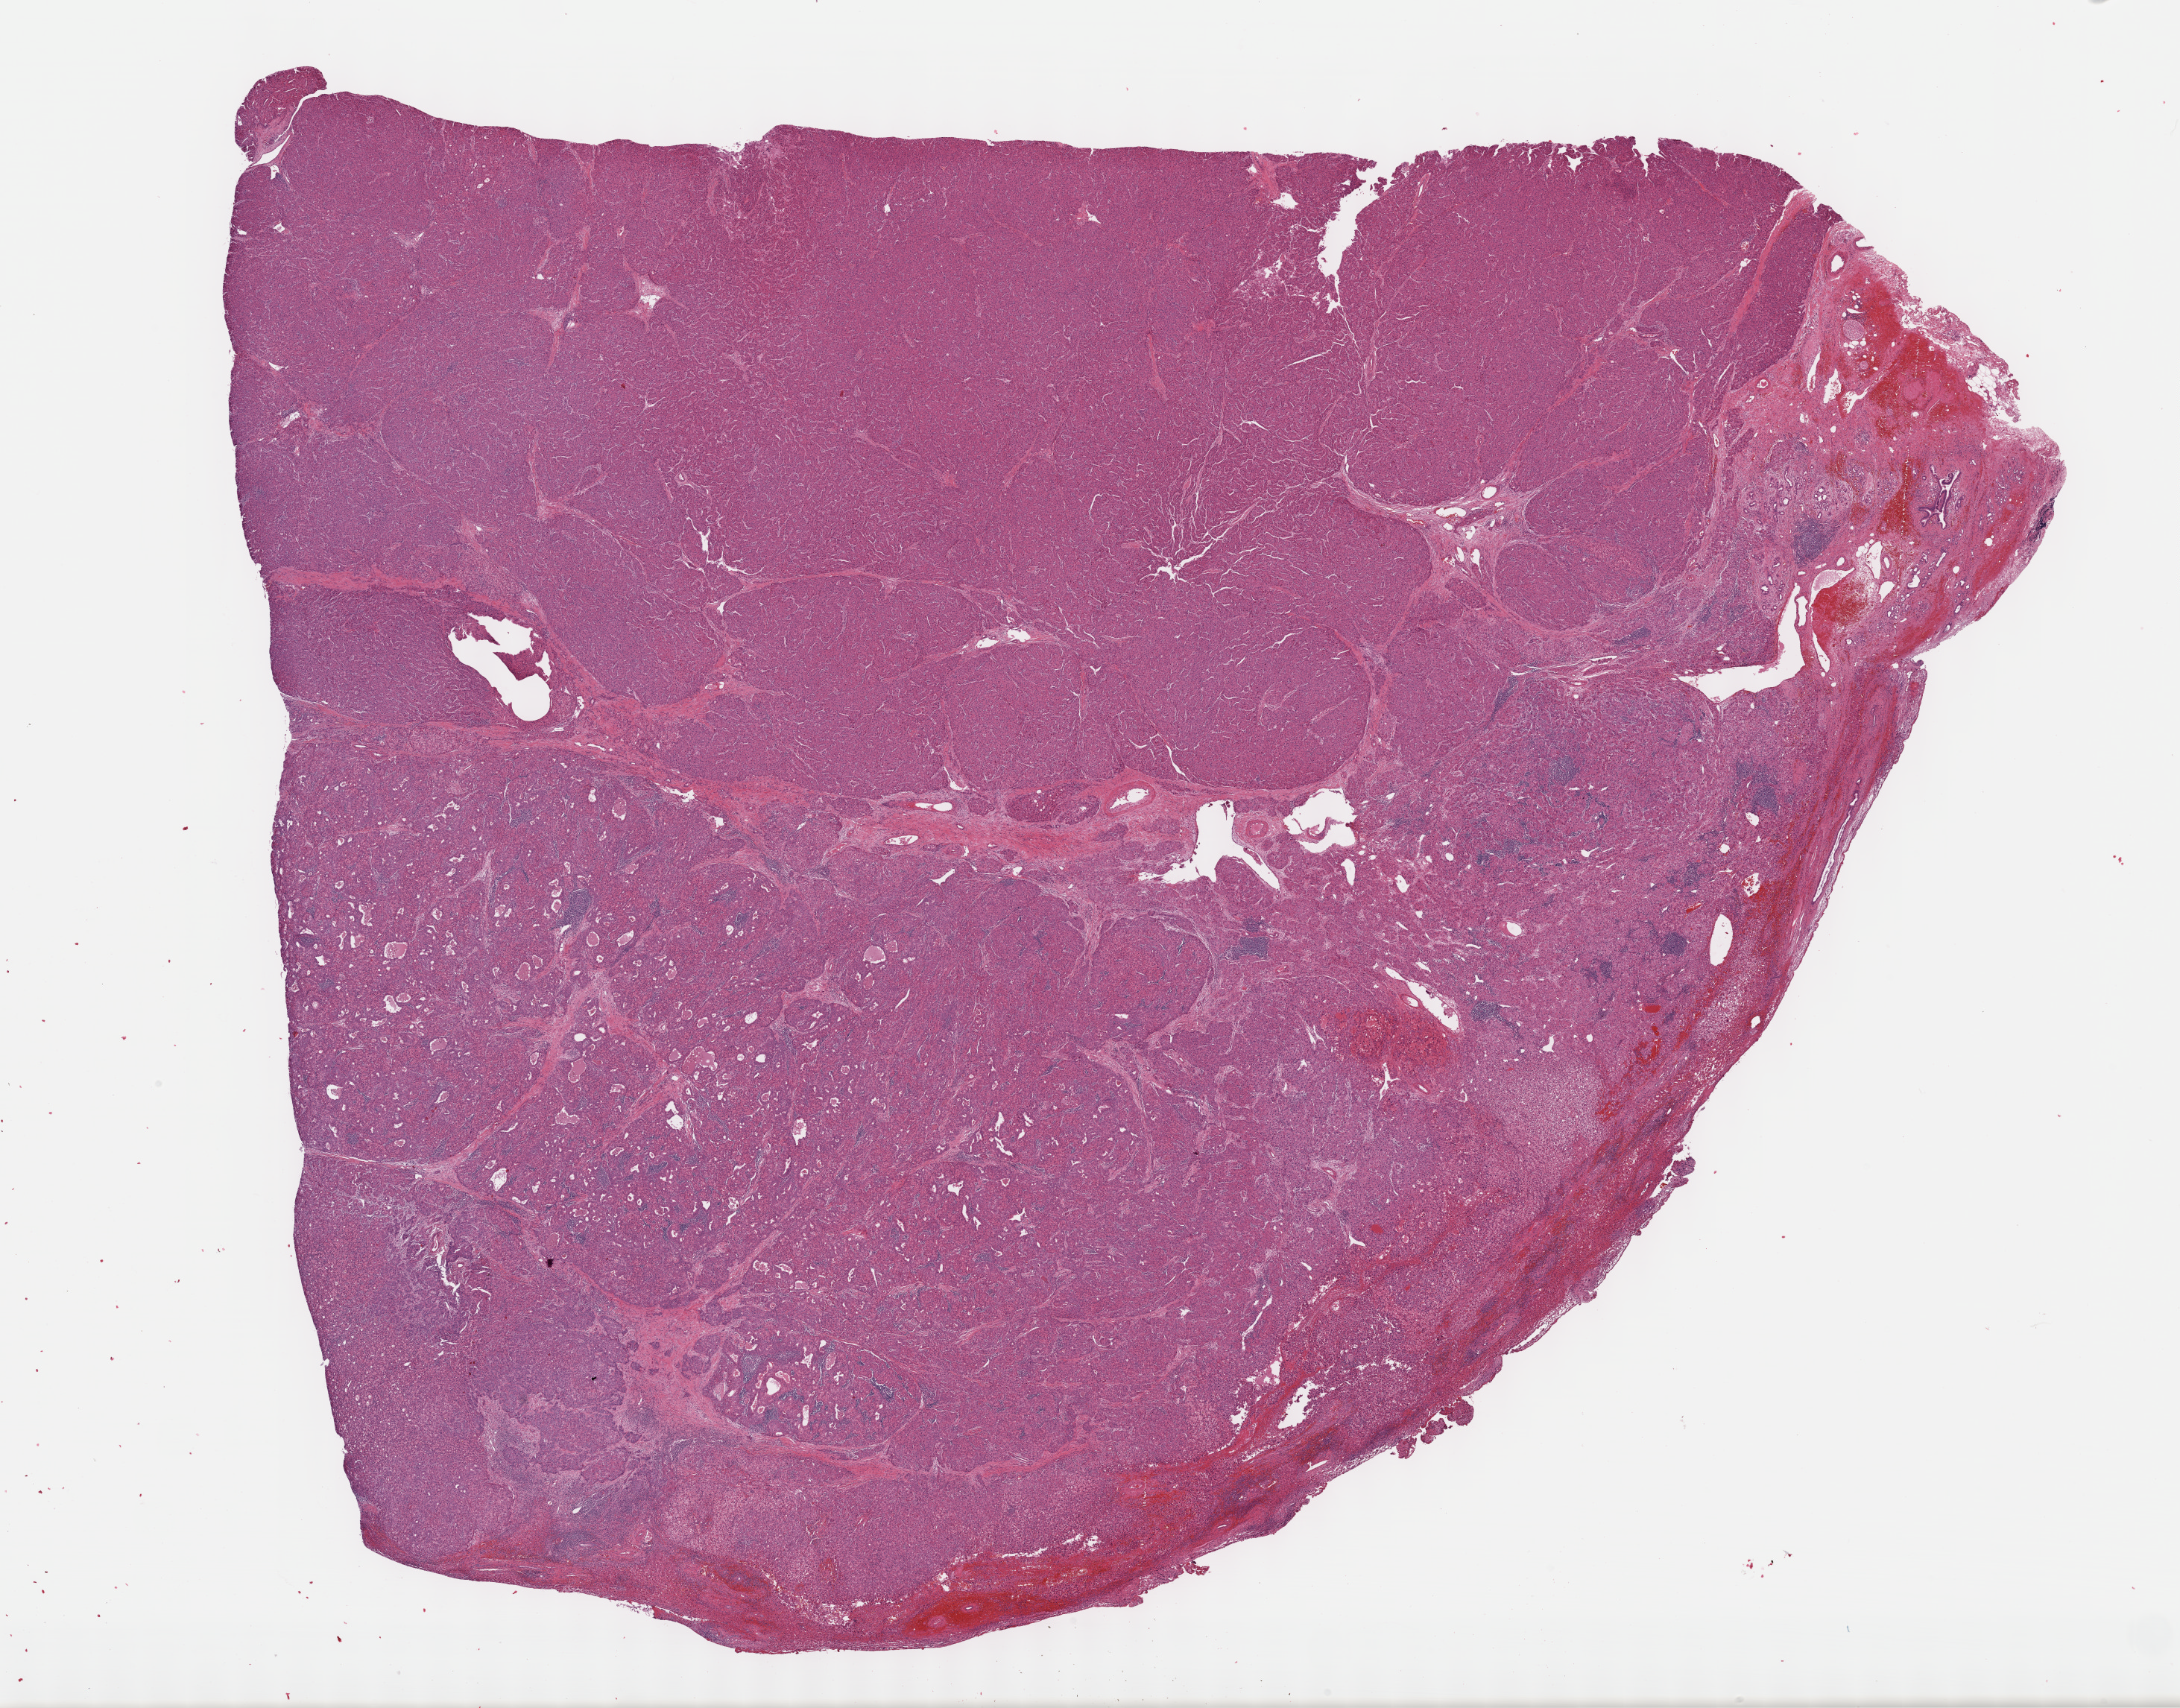
Whole-slide histology image, H&E — low-resolution overview of the scanned area, about 23.7 x 18.5 mm (slide scanned at 40x). Formalin-fixed paraffin-embedded (FFPE) diagnostic section. Sample: primary tumour, liver. Patient: male, age at initial diagnosis 65 years. Histologic grade: G1 (well differentiated).
Diagnosis: Hepatocellular carcinoma, NOS. TNM: T1 N0 M0. AJCC pathologic stage: I (6th edition).